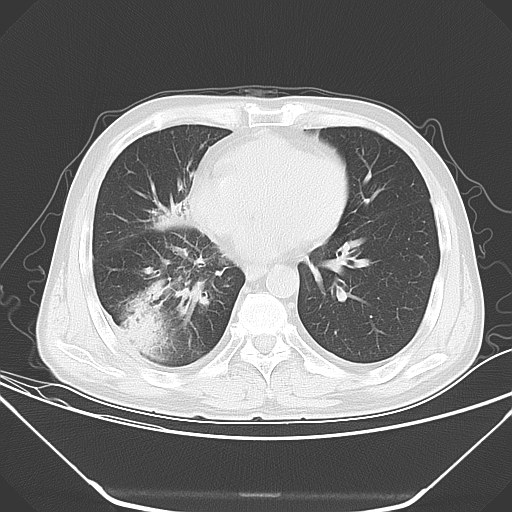
Chest CT, one axial slice; slice 19 of 52 in the series (ordered by position); 120 kVp; lung window (W 1500 / L -600 HU); 5 mm slice thickness; 512 × 512 image matrix, field of view 379 × 379 mm. Male patient, age 54 years. From the clinical record (not read from this slice): clinical TNM (as recorded): T2 N1 M0.
Outlined on this slice (rectangle marked by the reading radiologist):
- lung tumour (recorded histology: adenocarcinoma): box from (x=118, y=278) to (x=169, y=357) px